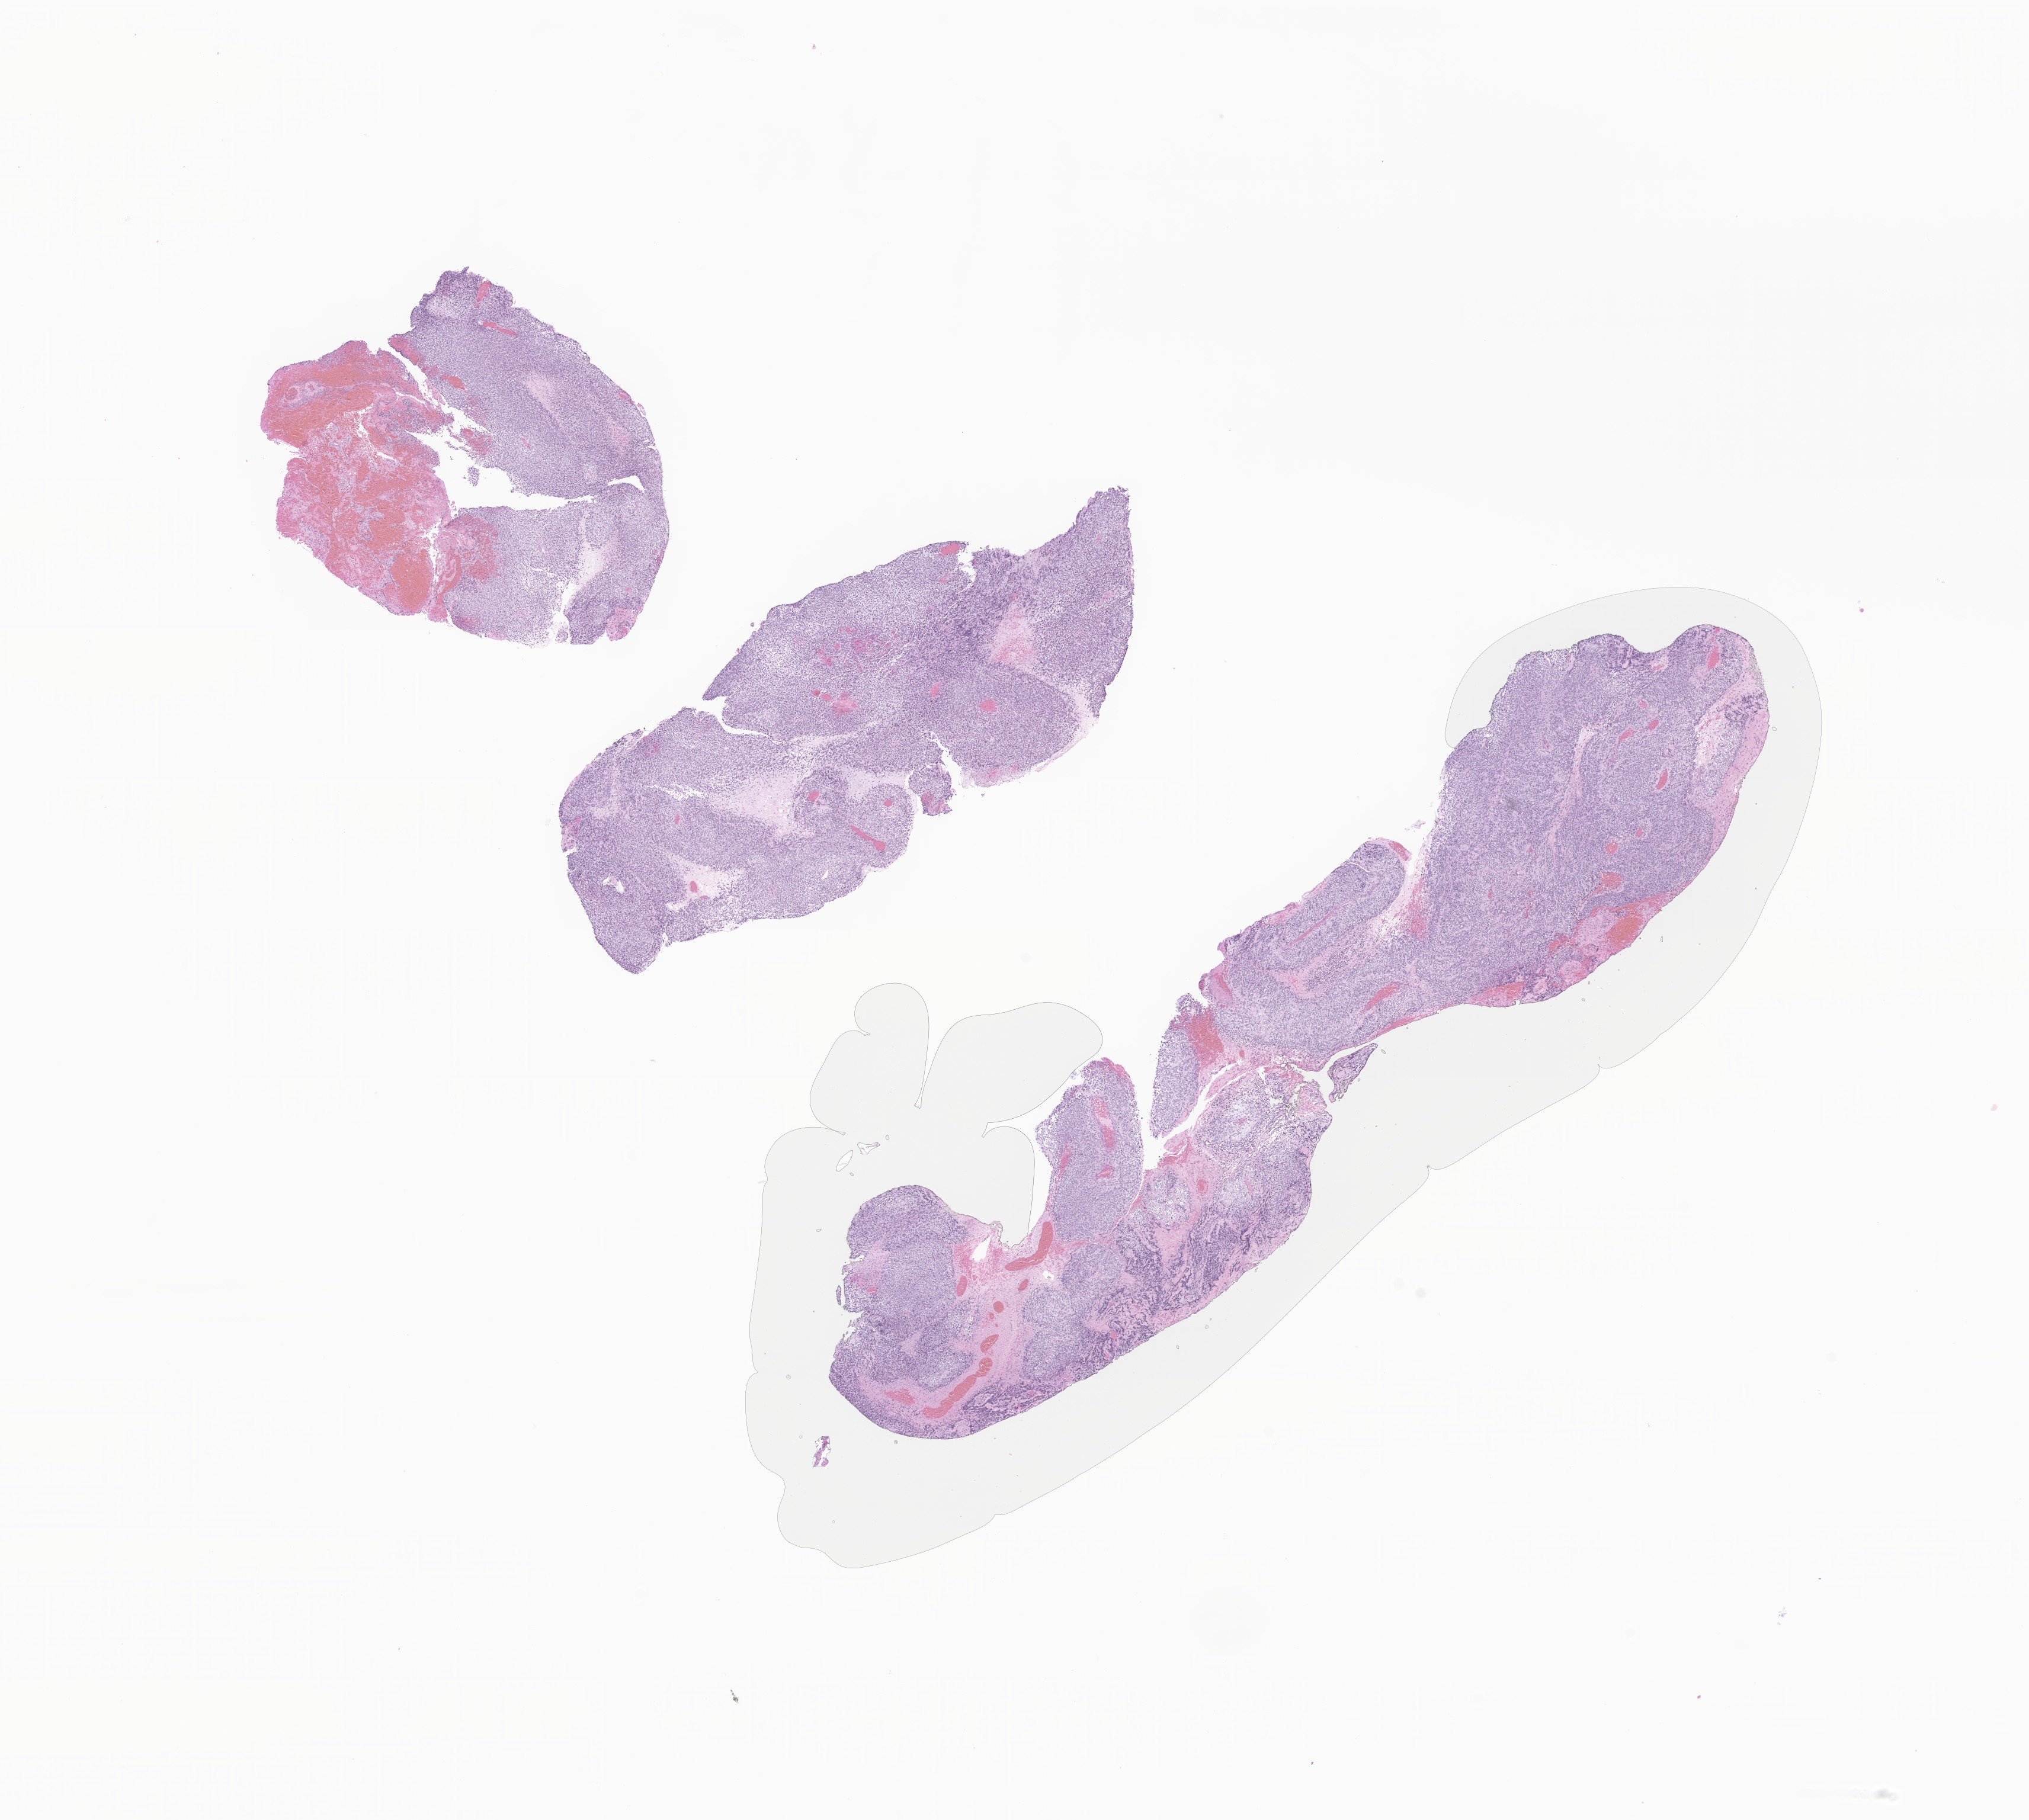
Digitized hematoxylin and eosin (H&E)-stained section of tumor tissue from the spinal cord, whole scanned area (about 14.4 x 13.0 mm) shown as a low-resolution overview; FFPE section. Female patient, age 93 months (7 years 9 months).
Diagnosis (ICD-O-3 morphology term): Astroblastoma.